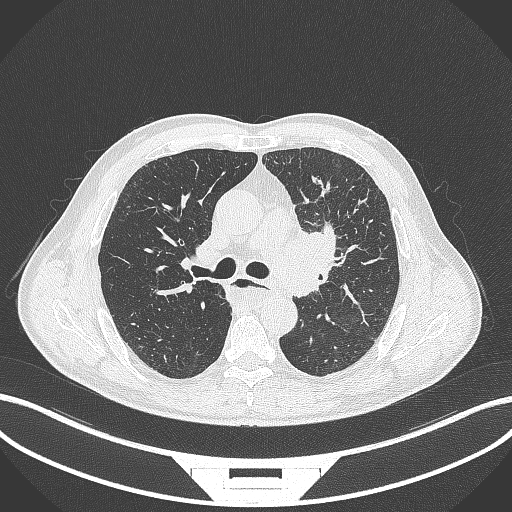
Chest CT, one axial slice. Position 240 of 411 along the scan axis. Reconstruction kernel B70f. 120 kVp. Lung window (W 1500 / L -600 HU). 1 mm slice thickness. 512 × 512 image matrix. Patient: male, 57 years. From the clinical record (not read from this slice): clinical TNM (as recorded): T2a N1 M0.
Outlined on this slice (rectangle marked by the reading radiologist):
- lung tumour (recorded histology: squamous cell carcinoma): bounding box (x1, y1, x2, y2) in pixels: (269, 216, 348, 304)